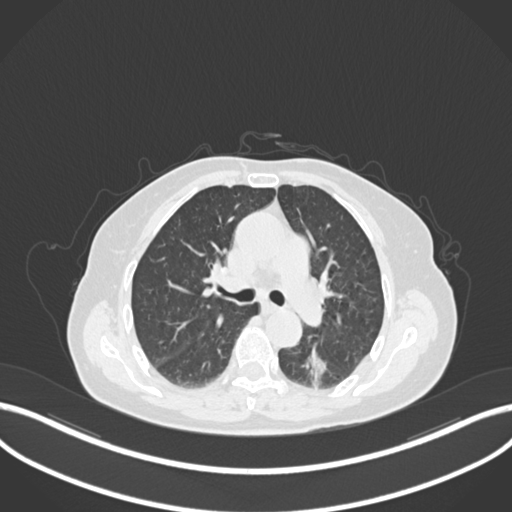
Chest CT, one axial slice; 120 kVp; lung window (W 1500 / L -600 HU); 512 × 512 image matrix, field of view 400 × 400 mm. Female patient, age 70 years. Case-level facts recorded for this patient, not image findings: clinical TNM (as recorded): T1c N0 M0.
Structures marked on this image (bounding box drawn by a radiologist):
- lung tumour (recorded histology: adenocarcinoma): bounding box <300,344,328,385> (left, top, right, bottom; pixels)